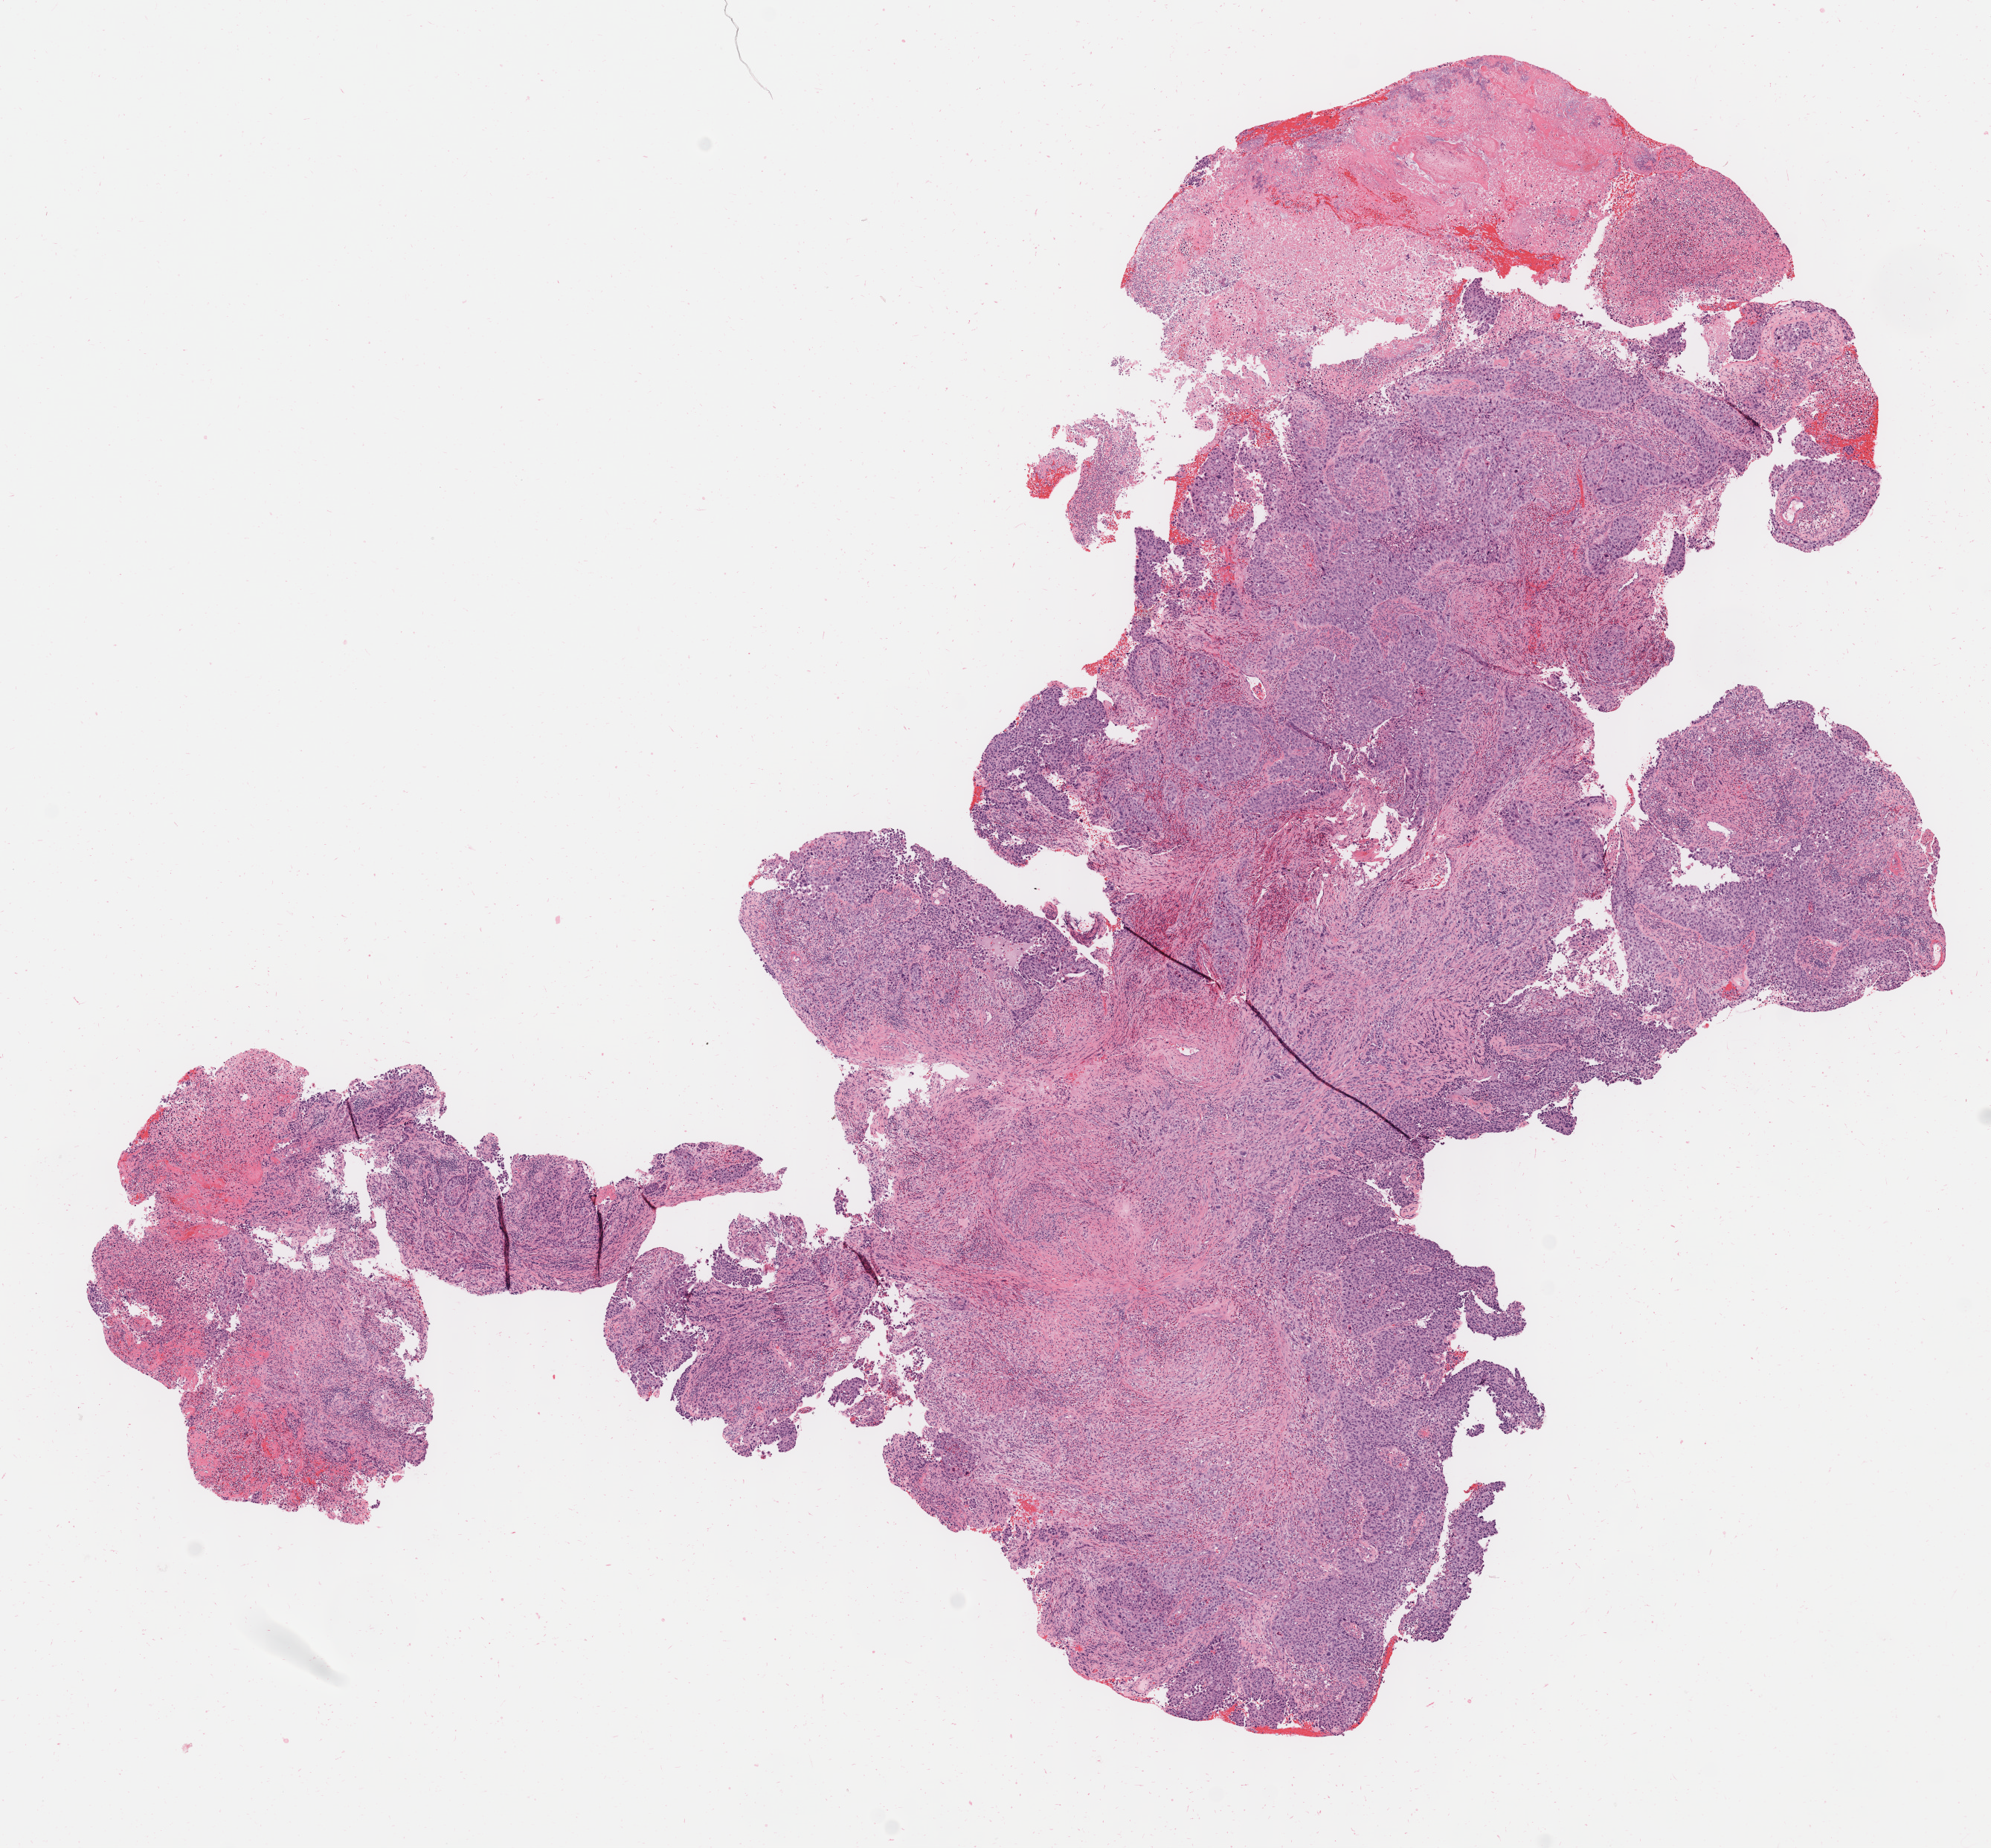
Digitized haematoxylin and eosin-stained section — shown as a low-resolution overview of the whole scanned area (about 10.7 x 9.9 mm); specimen: tumor tissue; site: cervix. Patient sex: female.
• diagnosis: Squamous cell carcinoma, large cell, nonkeratinizing, NOS